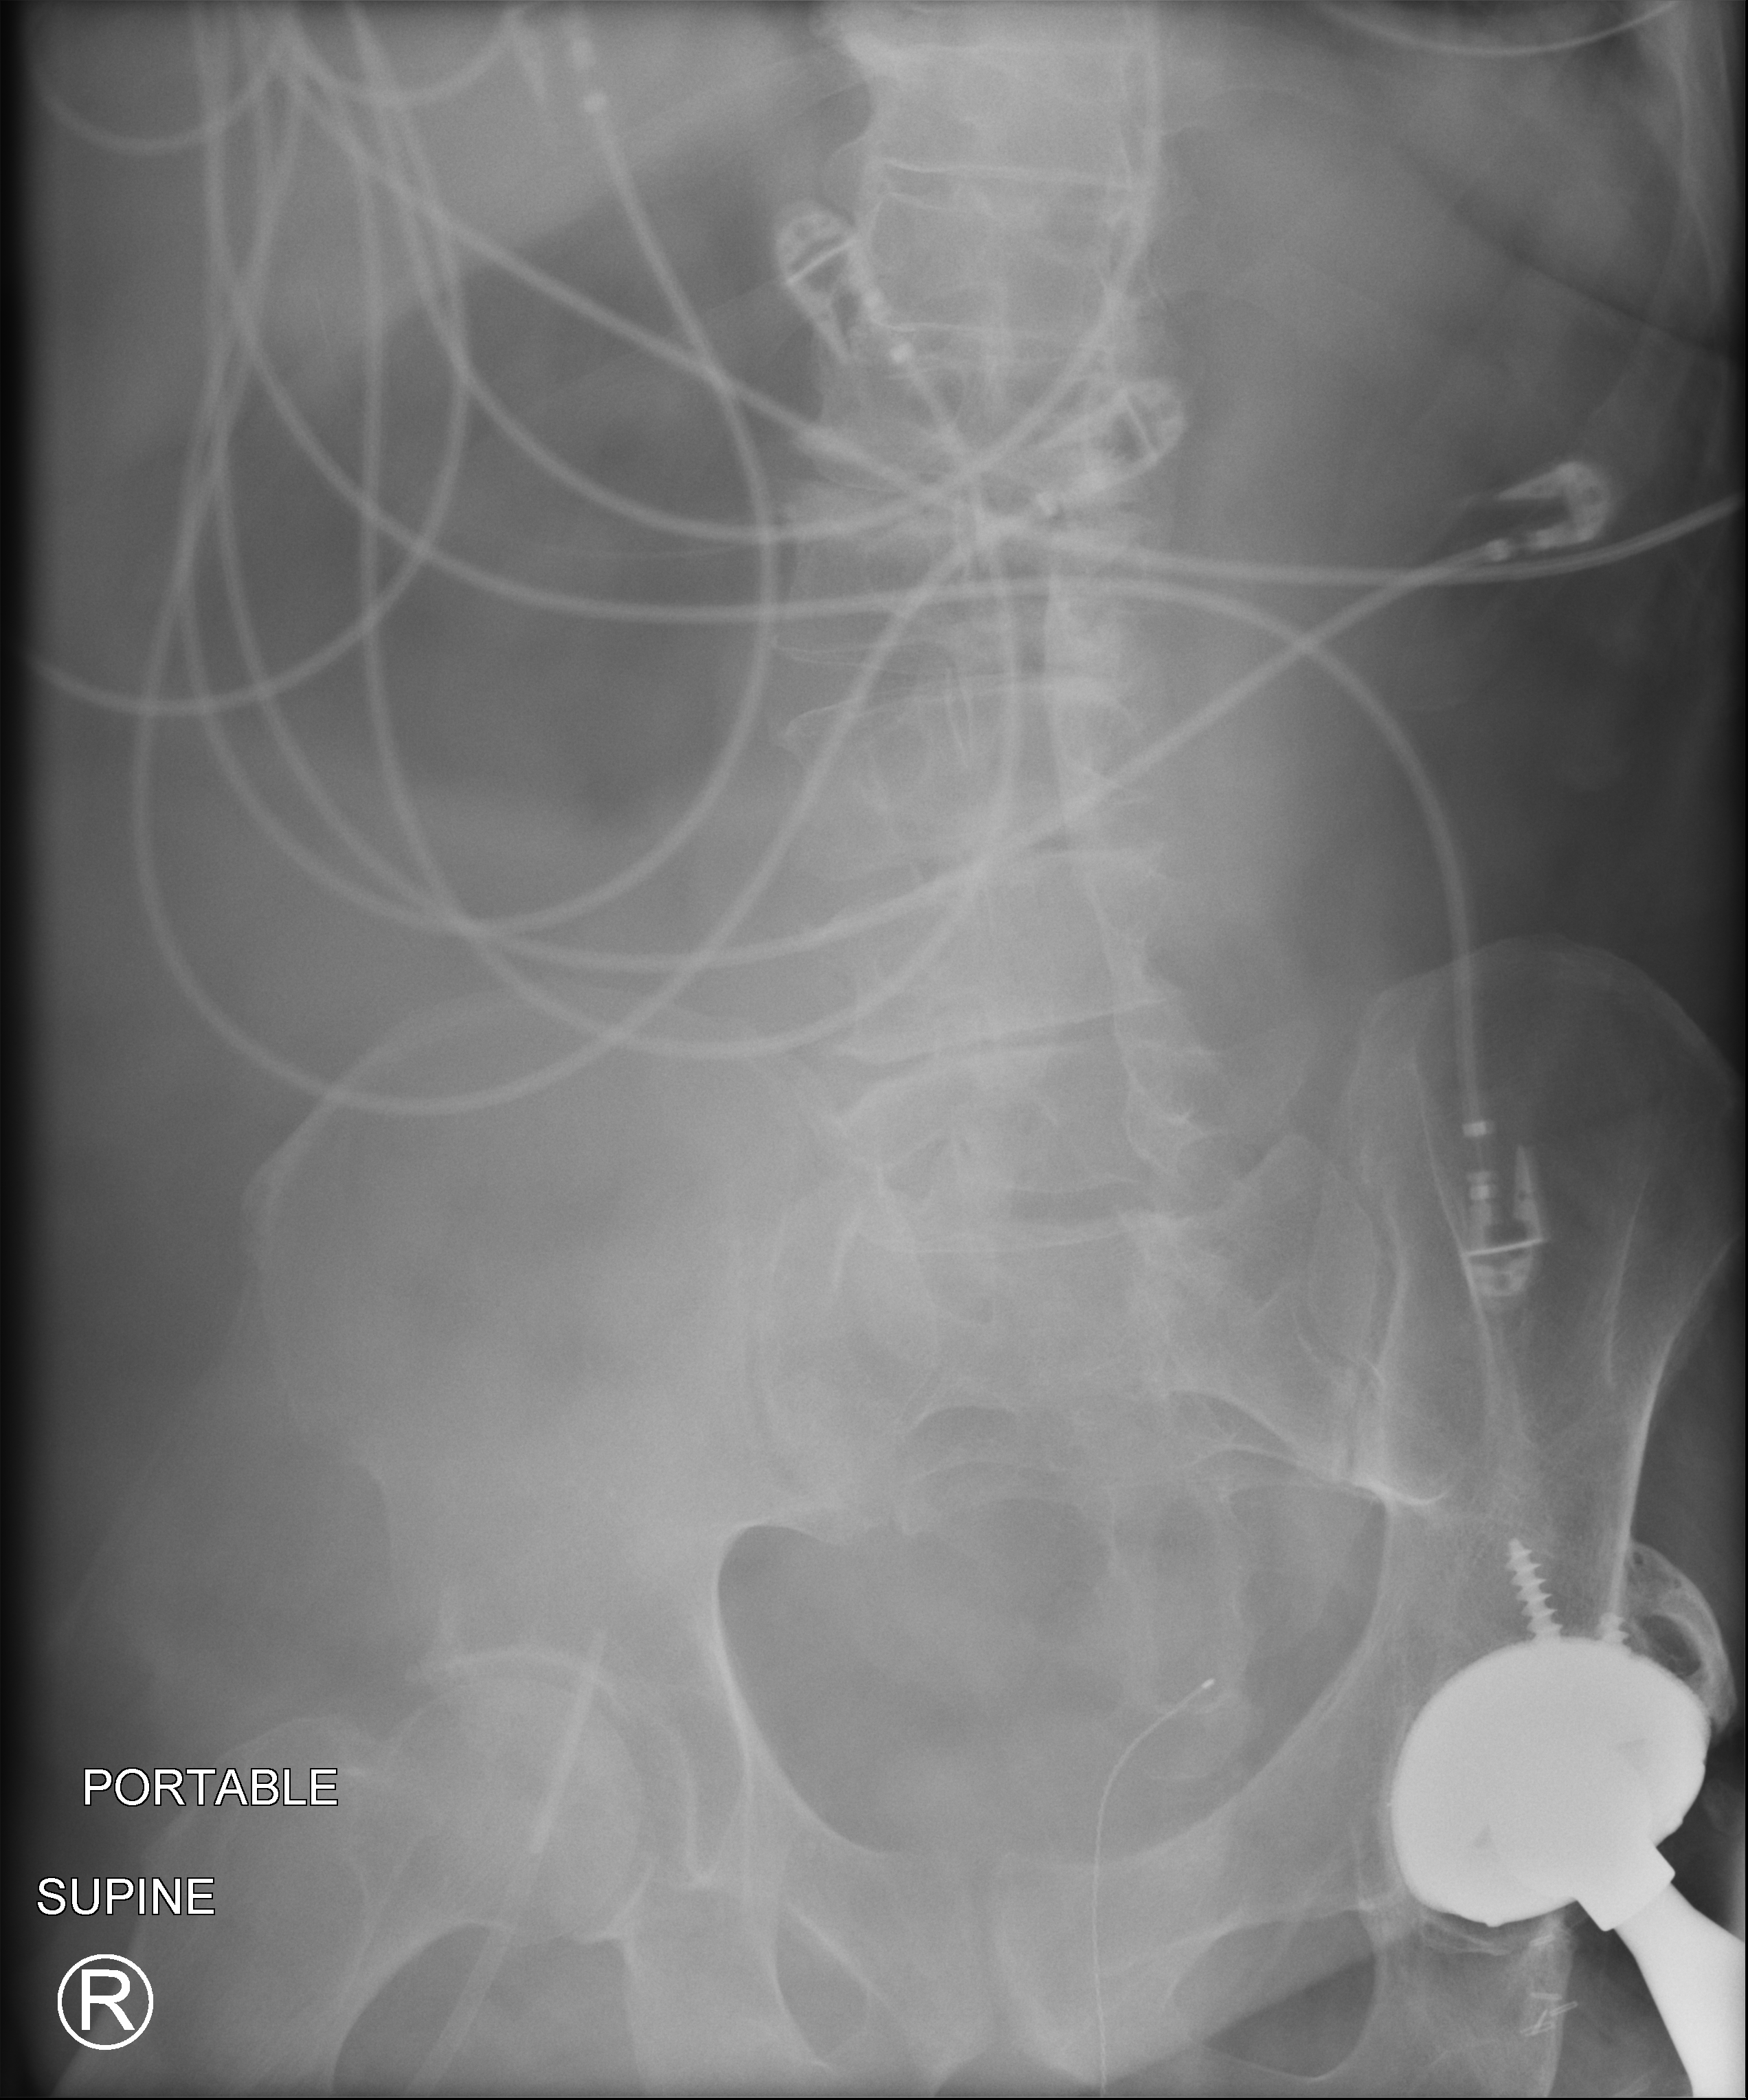
Bedside abdomen radiograph (computed radiography); anteroposterior (AP) projection. Male patient hospitalised with COVID-19, age 60–74 years.
From the hospital-stay record, not from the radiograph (when in the stay this image was taken is not recorded): diabetes (admission record): no.